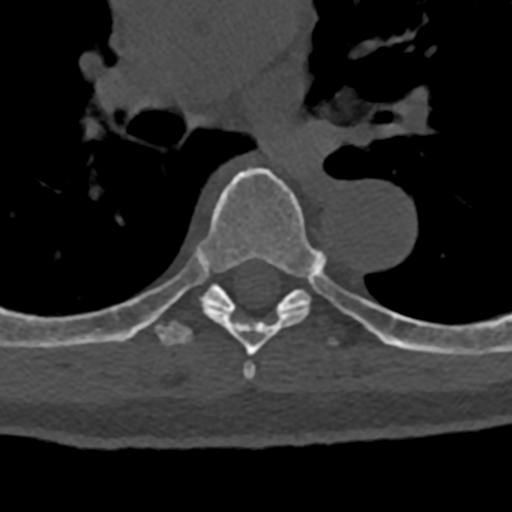
CT including the spine, one axial slice; slice 796 of 797 in the series (ordered by position); reconstruction kernel Br40s/3; 120 kVp; bone window (W 1800 / L 400 HU); 0.5 mm slice thickness; 512 × 512 image matrix. Patient: male, 74 years. From the clinical record (not read from this slice): primary cancer: renal; vertebrae with lytic lesions (as recorded): T10, L1, L2, L3, L4, L5.
Structures marked on this image (semi-automatic segmentation, software-assisted and operator-edited):
- T6 vertebra: box from (x=143, y=167) to (x=318, y=380) px
- T7 vertebra: (x=70, y=250)–(x=432, y=354)